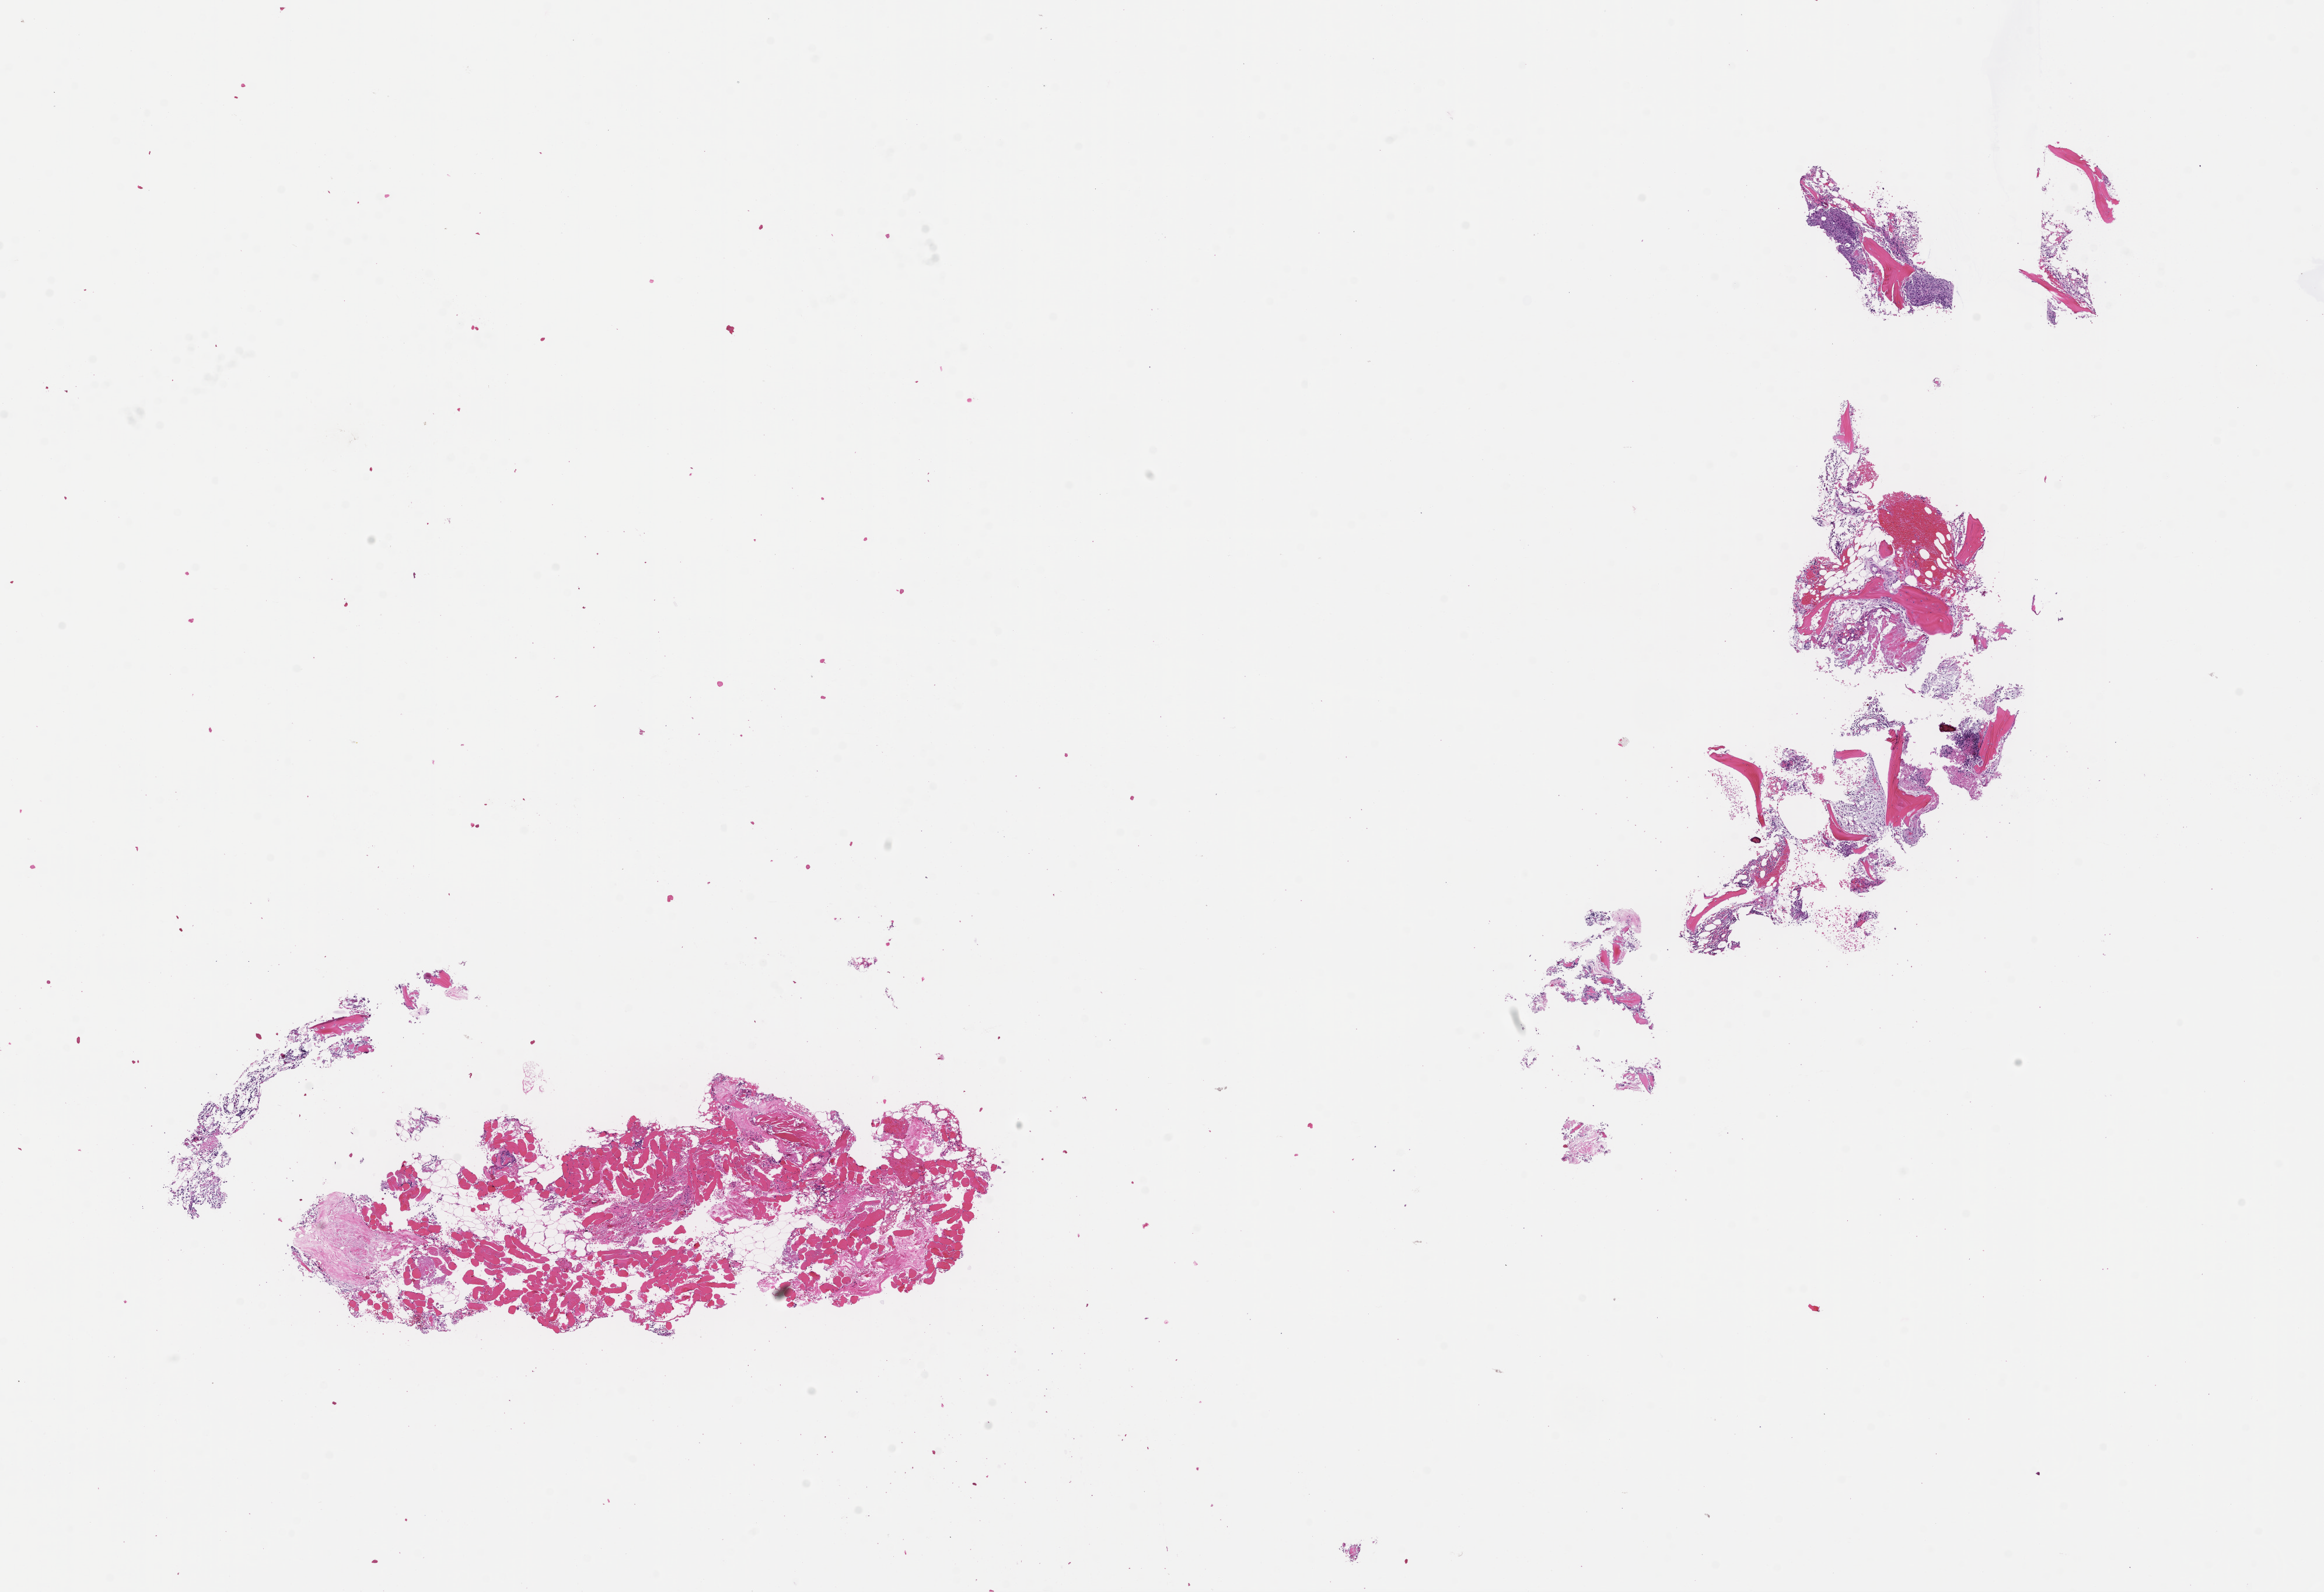
Whole-slide image, hematoxylin and eosin (H&E) stain — shown as a low-resolution overview of the whole scanned area (about 16.1 x 11.0 mm), formalin-fixed paraffin-embedded section, site: bone marrow. Patient: female.
- this section: primary tumor
- diagnosis: Plasma Cell Myeloma